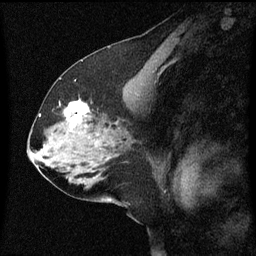
Breast MRI (dynamic contrast-enhanced), one sagittal slice; position 32 of 60 along the scan axis; dynamic contrast-enhanced series, image 2 of 3 at this slice position (ordered by acquisition); 1.5 T; TE 4.2 ms, TR 8 ms; 2 mm slice thickness; 256 × 256 image matrix, field of view 200 × 200 mm. Patient: female, 58 years.
Structures marked on this image (semi-automatically segmented with operator editing):
- analysis volume of interest (the breast-tissue region the enhancement analysis was run in; not a lesion): bounding box <56,100,95,137> (left, top, right, bottom; pixels)
- tumour enhancement mask (voxels above the 70 % enhancement threshold inside the analysis volume of interest): <66,102,91,123>